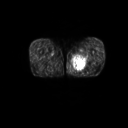
FDG PET of an extremity soft-tissue mass (from a PET/CT study), one axial slice; 3.27 mm slice thickness; 128 × 128 image matrix, field of view 600 × 600 mm. Patient: male, 59 years. From the clinical record (not read from this slice): histological type: pleiomorphic liposarcoma; grade: high; site of the primary tumour: left thigh.
Outlined on this slice (expert contour drawn on MRI and transferred to this co-registered scan by the dataset authors):
- gross tumour volume including surrounding oedema: bounding box <73,53,90,72> (left, top, right, bottom; pixels)
- gross tumour volume (mass): <74,59,87,71>